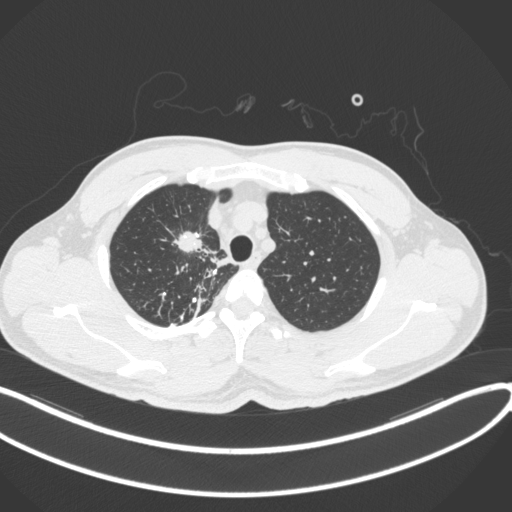
Chest CT, one axial slice; position 308 of 391 along the scan axis; reconstruction kernel B31f; lung window (W 1500 / L -600 HU); 512 × 512 image matrix, field of view 400 × 400 mm. Male patient, age 48 years. Case-level facts recorded for this patient, not image findings: clinical TNM (as recorded): T1c N1 M1.
Structures marked on this image (rectangle marked by the reading radiologist):
- lung tumour (recorded histology: adenocarcinoma): bounding box [x1, y1, x2, y2] px = [169, 228, 205, 254]